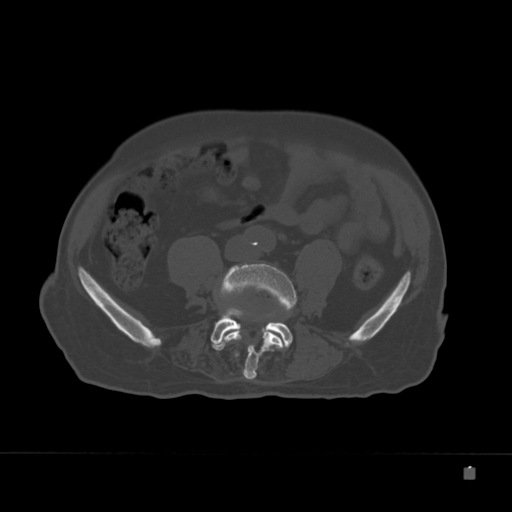
CT including the spine, one axial slice. Position 34 of 332 along the scan axis. 120 kVp. Bone window (W 1800 / L 400 HU). 512 × 512 image matrix. Male patient, age 72 years. Case-level facts recorded for this patient, not image findings: primary cancer: skeletal.
Annotated regions visible in this slice (semi-automatically segmented with operator editing):
- L4 vertebra: bounding box (x1, y1, x2, y2) in pixels: (223, 263, 297, 381)
- L5 vertebra: (211, 308, 293, 351)